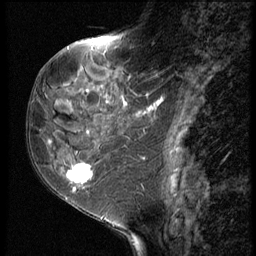
Breast MRI (dynamic contrast-enhanced), one sagittal slice. Position 25 of 62 along the scan axis. 3 images stored at this slice position (order not interpretable as contrast timing). 1.5 T. TE 4.2 ms, TR 9 ms. 2.5 mm slice thickness. 256 × 256 image matrix, field of view 180 × 180 mm. Female patient, age 50 years. Case-level facts recorded for this patient, not image findings: setting: breast cancer imaged before/during neoadjuvant chemotherapy; receptor status: HR-positive, HER2-negative.
Annotated regions visible in this slice (semi-automatic segmentation, software-assisted and operator-edited):
- analysis volume of interest (the breast-tissue region the enhancement analysis was run in; not a lesion): box from (x=32, y=91) to (x=118, y=209) px
- tumour enhancement mask (voxels above the 140 % enhancement threshold inside the analysis volume of interest): (x=67, y=163)–(x=94, y=190)